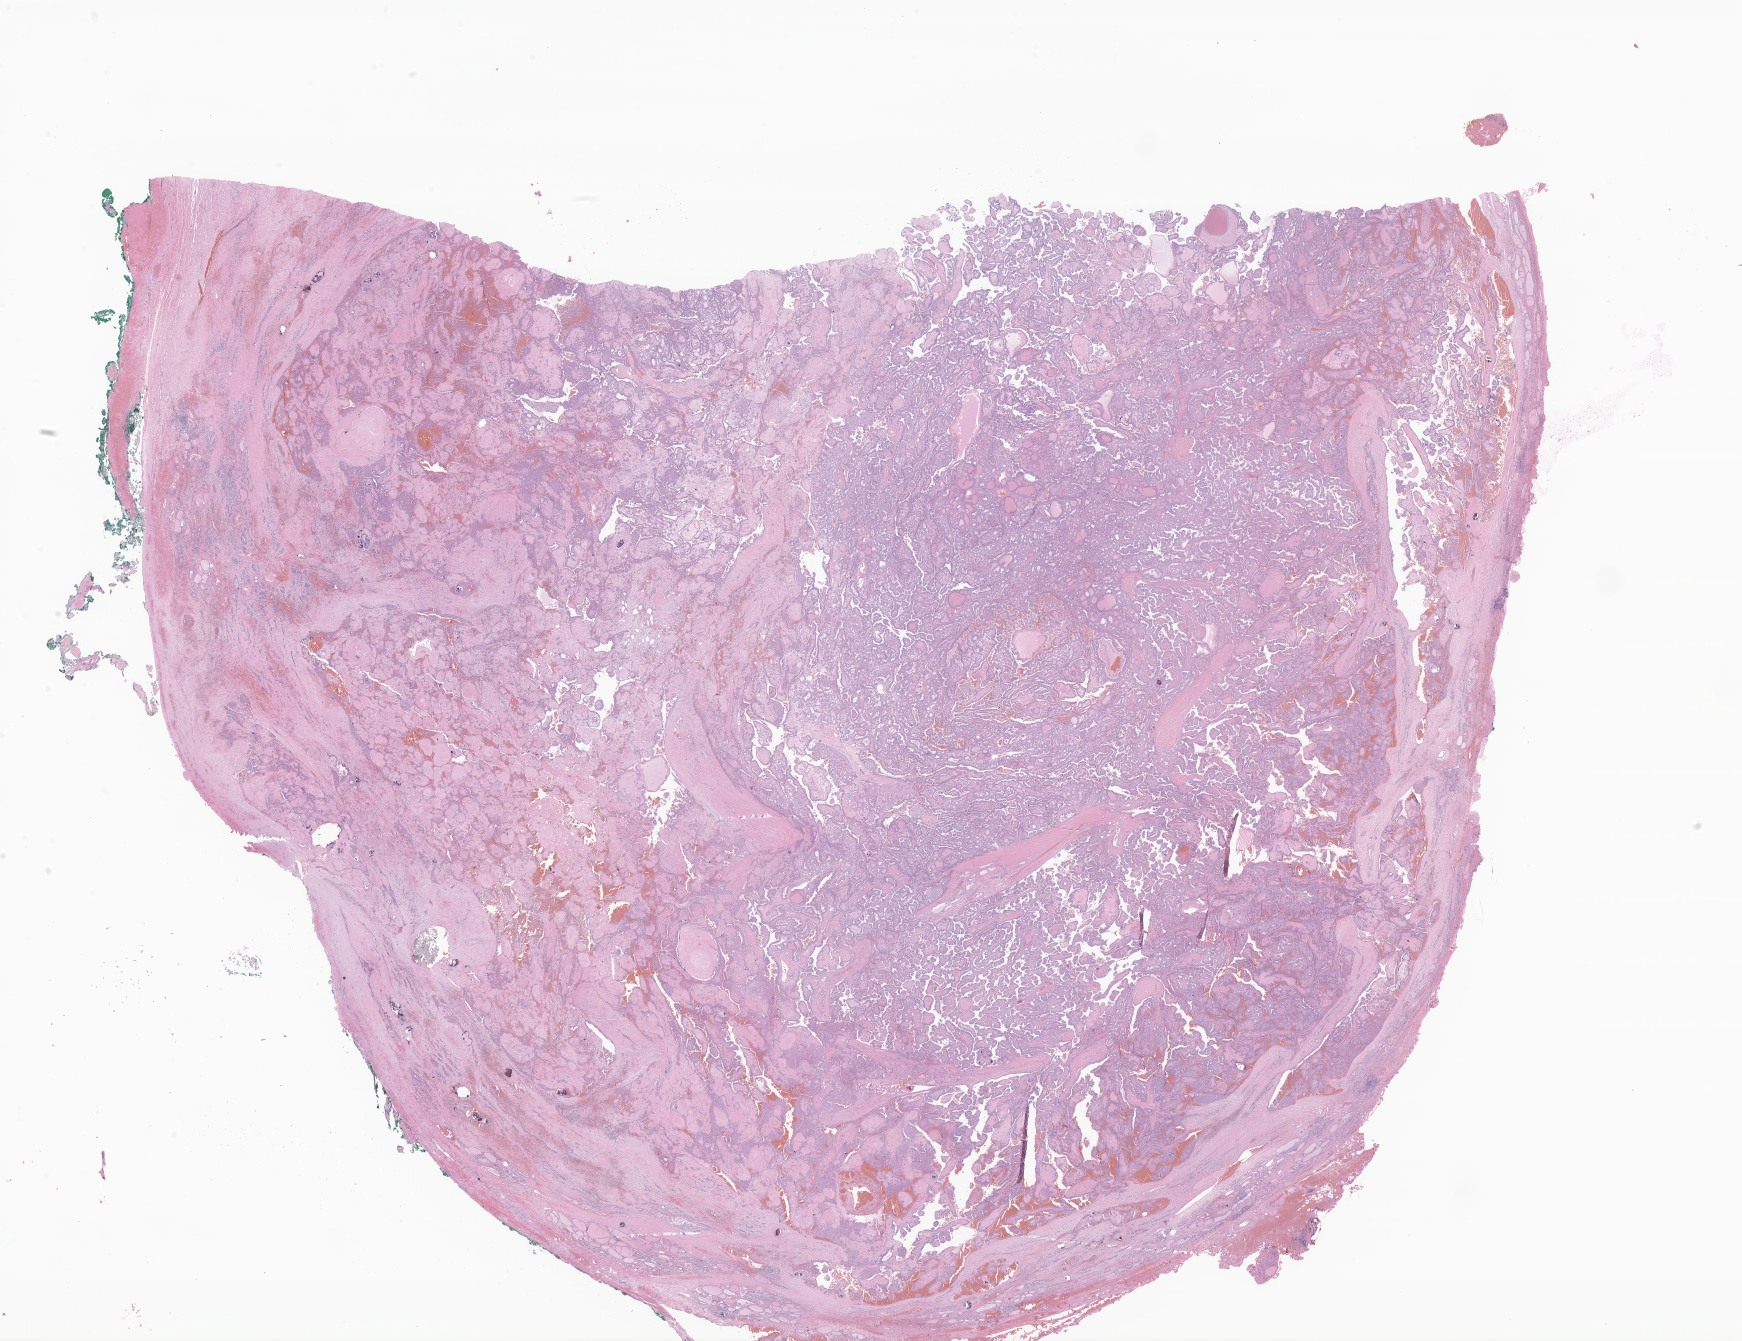
H&E whole-slide image of tumor tissue from the thyroid — shown as a low-resolution overview of the whole scanned area (about 29.4 x 22.6 mm); formalin-fixed, paraffin-embedded (FFPE) tissue. Patient: male, age 192 months.
- diagnosis (ICD-O-3 morphology term): Papillary adenocarcinoma, NOS